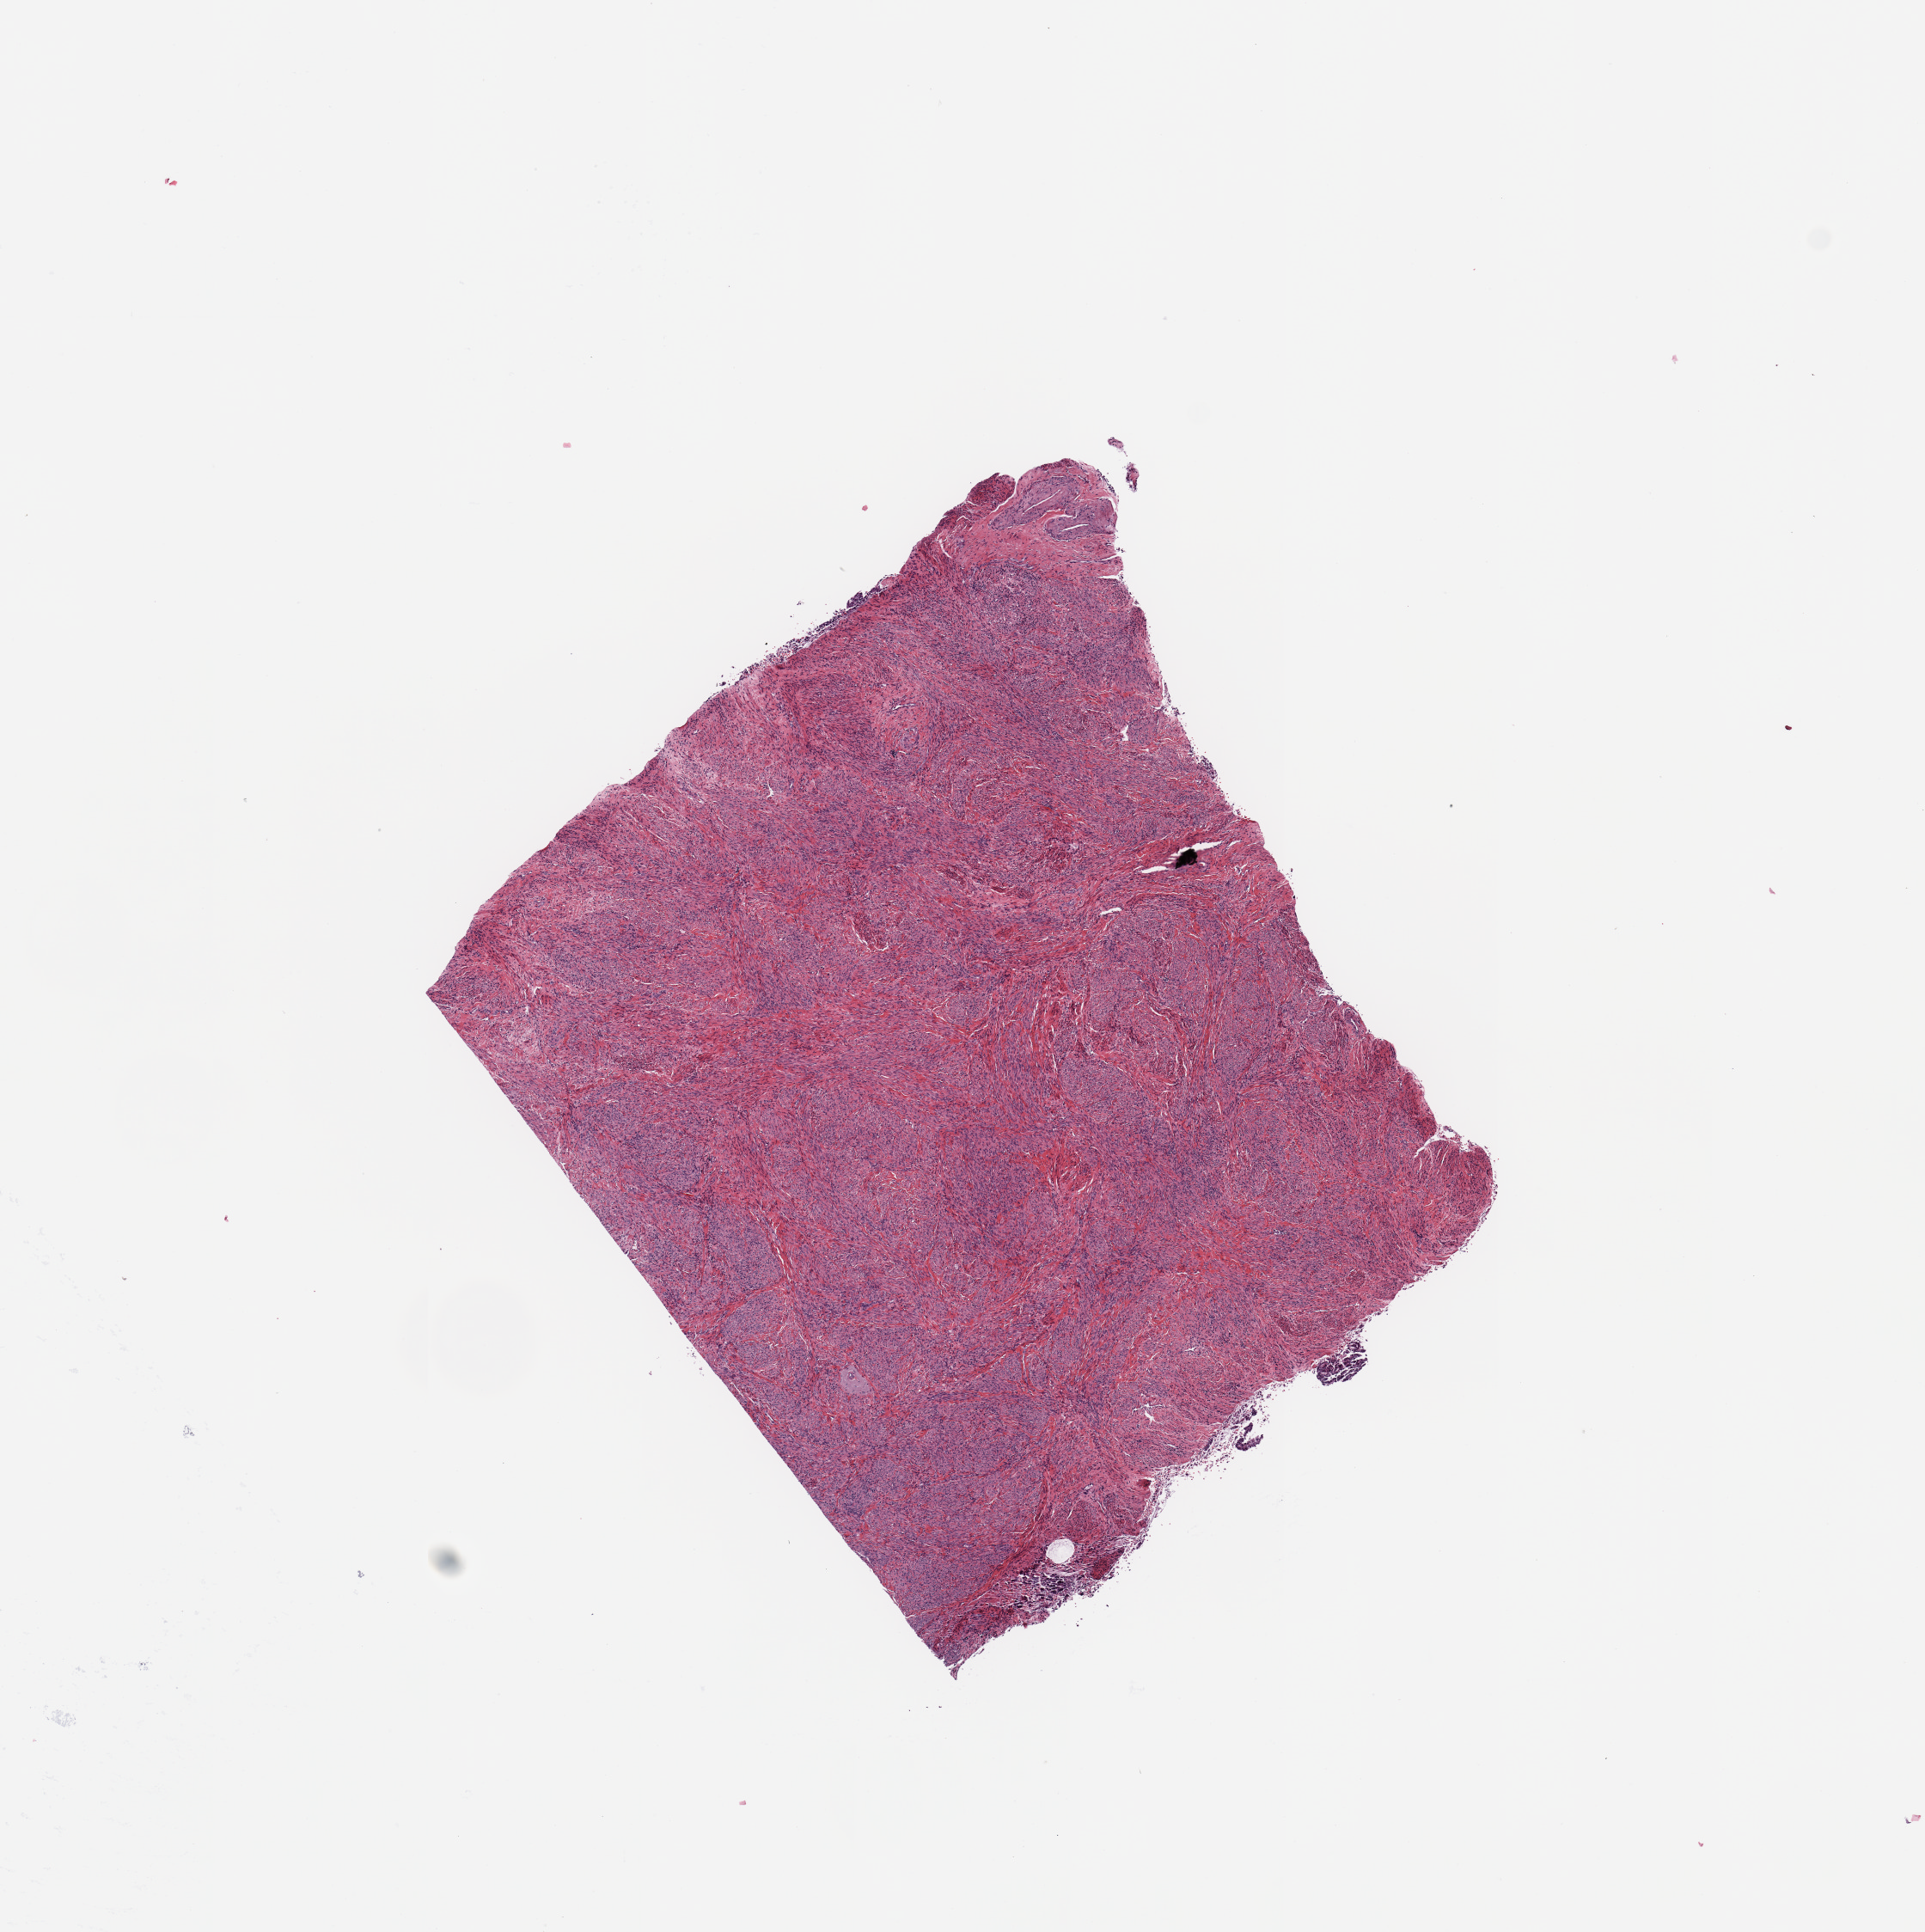
Digitized H&E tissue section (whole slide) — low-resolution overview of the scanned area, about 8.9 x 8.9 mm (slide scanned at 20x). Uterus, normal (non-tumour) tissue. Female, 84 y/o.
This section: normal (non-tumour) tissue from the same patient. Patient diagnosis: Endometrioid adenocarcinoma, NOS.